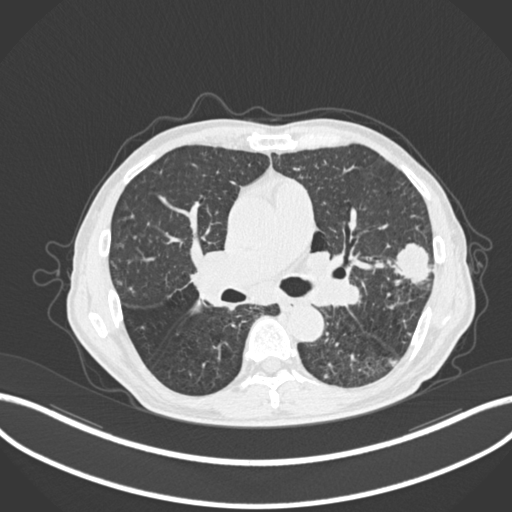
Chest CT, one axial slice; position 139 of 287 along the scan axis; 120 kVp; lung window (W 1500 / L -600 HU); 1 mm slice thickness; 512 × 512 image matrix. Patient: male, 74 years. From the clinical record (not read from this slice): clinical TNM (as recorded): T2a N1 M0.
Structures marked on this image (bounding box drawn by a radiologist):
- lung tumour (recorded histology: adenocarcinoma): box from (x=383, y=242) to (x=433, y=292) px